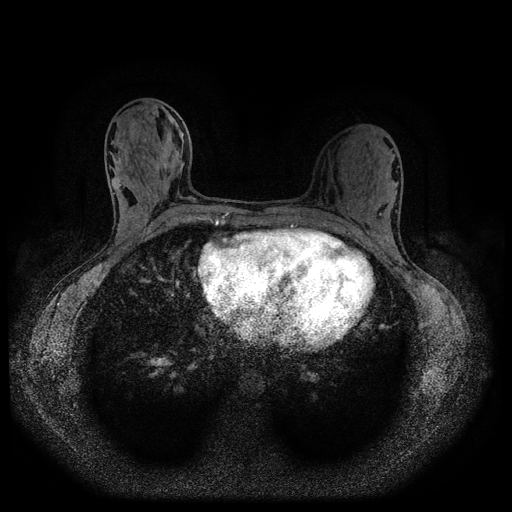
Breast MRI (dynamic contrast-enhanced, multi-phase), one axial slice. Position 45 of 116 along the scan axis. Dynamic contrast-enhanced series, time point 2 of 5 at this slice position (early post-contrast). 1.5 T. TE 2.7 ms, TR 5.4 ms. 512 × 512 image matrix, field of view 330 × 330 mm. Patient: female, 32 years.
Outlined on this slice (semi-automatic segmentation, software-assisted and operator-edited):
- breast lesion (labelled benign in the annotation): bounding box [x1, y1, x2, y2] px = [127, 117, 140, 141]